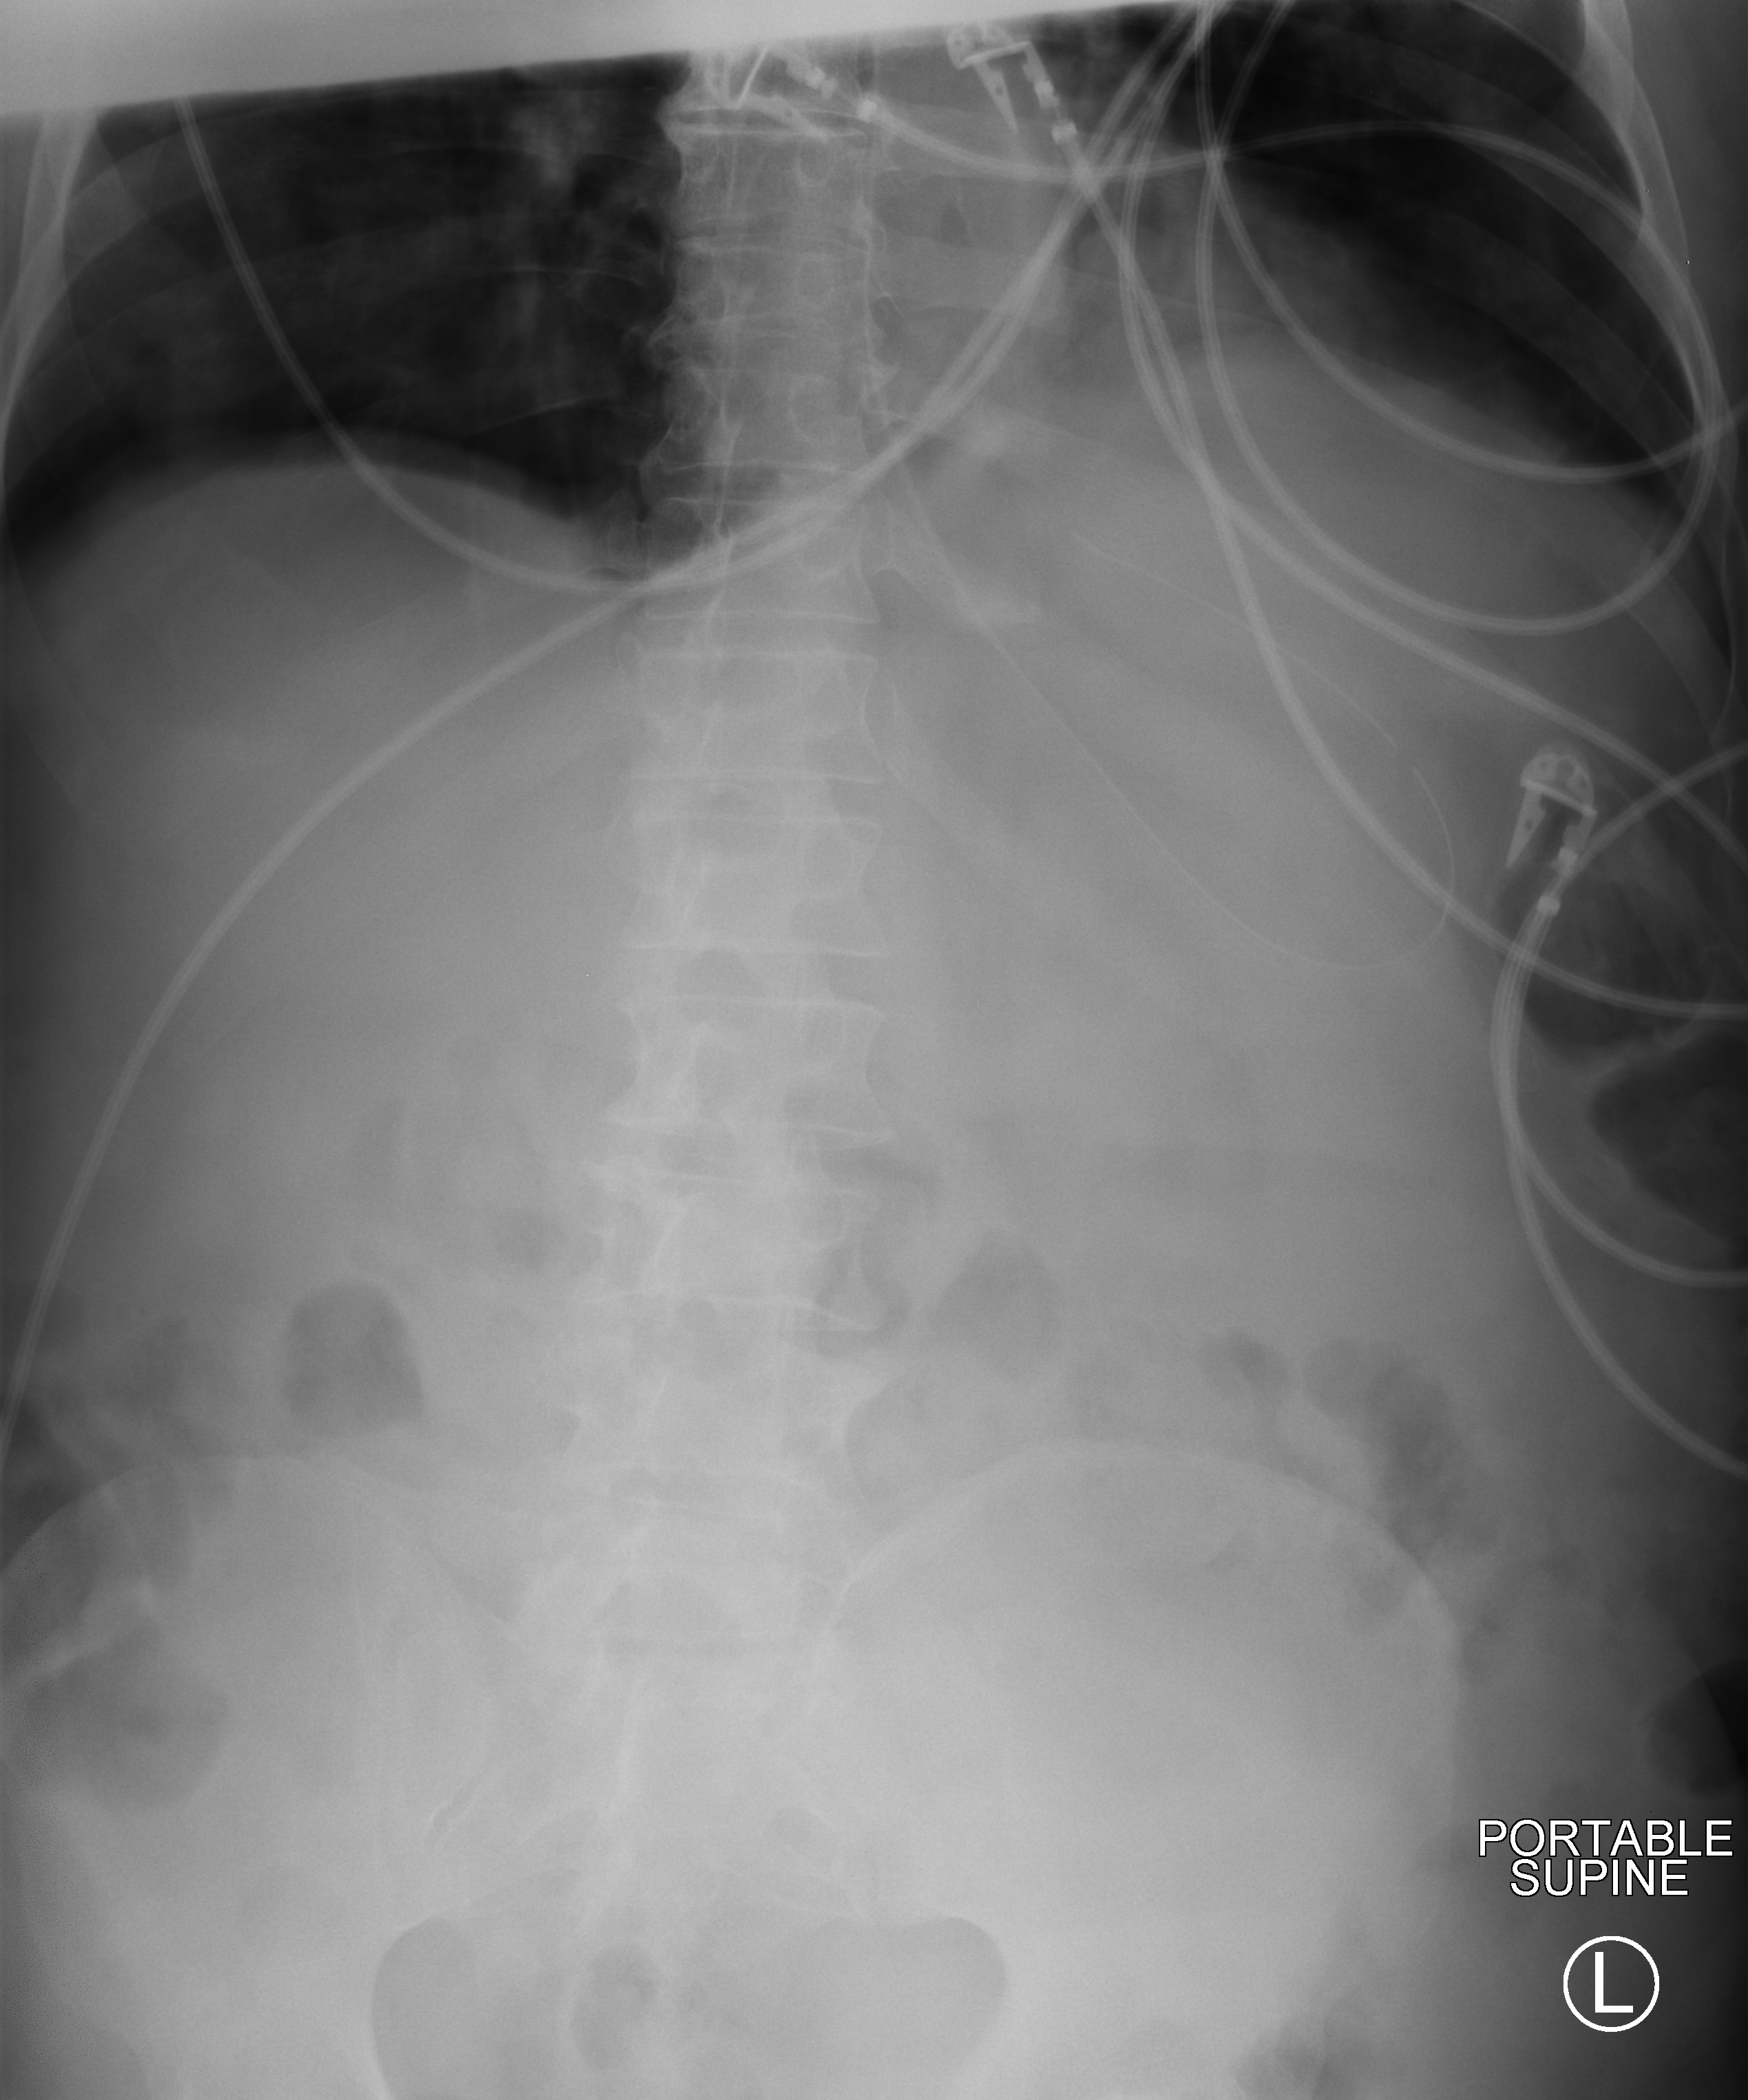
Bedside abdomen radiograph (computed radiography); anteroposterior (AP) projection. Male patient hospitalised with COVID-19, age 60–74 years.
Hospital-stay facts (about this admission, not read from this image; timing relative to this image not recorded): admitted to intensive care during this hospital stay: yes.